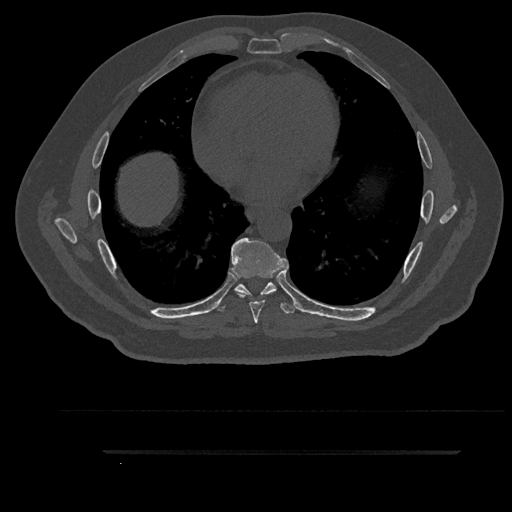
CT including the spine, one axial slice. Slice 505 of 797 in the series (ordered by position). Reconstruction kernel Br40s/3. 120 kVp. Bone window (W 1800 / L 400 HU). 0.5 mm slice thickness. 512 × 512 image matrix, field of view 432 × 432 mm. Male patient, age 63 years. From the clinical record (not read from this slice): primary cancer: renal.
Annotated regions visible in this slice (semi-automatic segmentation, software-assisted and operator-edited):
- T6 vertebra: box from (x=242, y=293) to (x=269, y=295) px
- T7 vertebra: (x=230, y=238)–(x=289, y=324)
- T8 vertebra: (x=215, y=248)–(x=299, y=314)